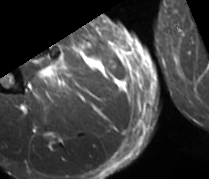
MRI of an extremity soft-tissue mass, one axial slice. Position 23 of 89 along the scan axis. STIR. MR volume resampled by the dataset authors to the PET/CT grid (not the native acquisition matrix). 3.27 mm slice thickness. 209 × 179 image matrix. Male patient. Case-level facts recorded for this patient, not image findings: histological type: undifferentiated - pleiomorphic; grade: high; site of the primary tumour: right thigh.
Annotated regions visible in this slice (expert contour drawn on MRI and transferred to this co-registered scan by the dataset authors):
- gross tumour volume including surrounding oedema: bounding box (x1, y1, x2, y2) in pixels: (37, 62, 102, 88)